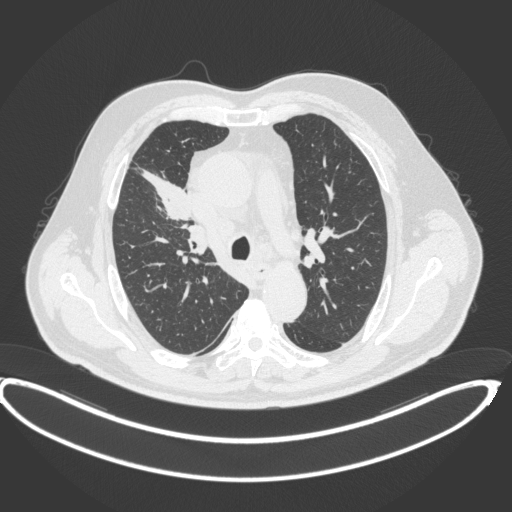
Chest CT, one axial slice. Slice 280 of 395 in the series (ordered by position). Reconstruction kernel B31f. 120 kVp. Lung window (W 1500 / L -600 HU). 1 mm slice thickness. 512 × 512 image matrix, field of view 448 × 448 mm. Patient: male, 62 years. Case-level facts recorded for this patient, not image findings: clinical TNM (as recorded): T1c N3 M1c.
Annotated regions visible in this slice (bounding box drawn by a radiologist):
- lung tumour (recorded histology: adenocarcinoma): bounding box [x1, y1, x2, y2] px = [137, 168, 193, 223]